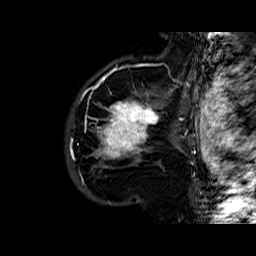
Breast MRI (dynamic contrast-enhanced), one sagittal slice; slice 45 of 60 in the series (ordered by position); dynamic contrast-enhanced series, time point 2 of 6 at this slice position (early post-contrast); 1.5 T; TE 6.4 ms, TR 32.8 ms; 4 mm slice thickness; 256 × 256 image matrix. Female patient. From the clinical record (not read from this slice): setting: breast cancer imaged before/during neoadjuvant chemotherapy; receptor status: HR-positive, HER2-negative.
Outlined on this slice (semi-automatic segmentation, software-assisted and operator-edited):
- analysis volume of interest (the breast-tissue region the enhancement analysis was run in; not a lesion): bounding box [x1, y1, x2, y2] px = [87, 77, 163, 177]
- tumour enhancement mask (voxels above the 100 % enhancement threshold inside the analysis volume of interest): [96, 78, 160, 159]